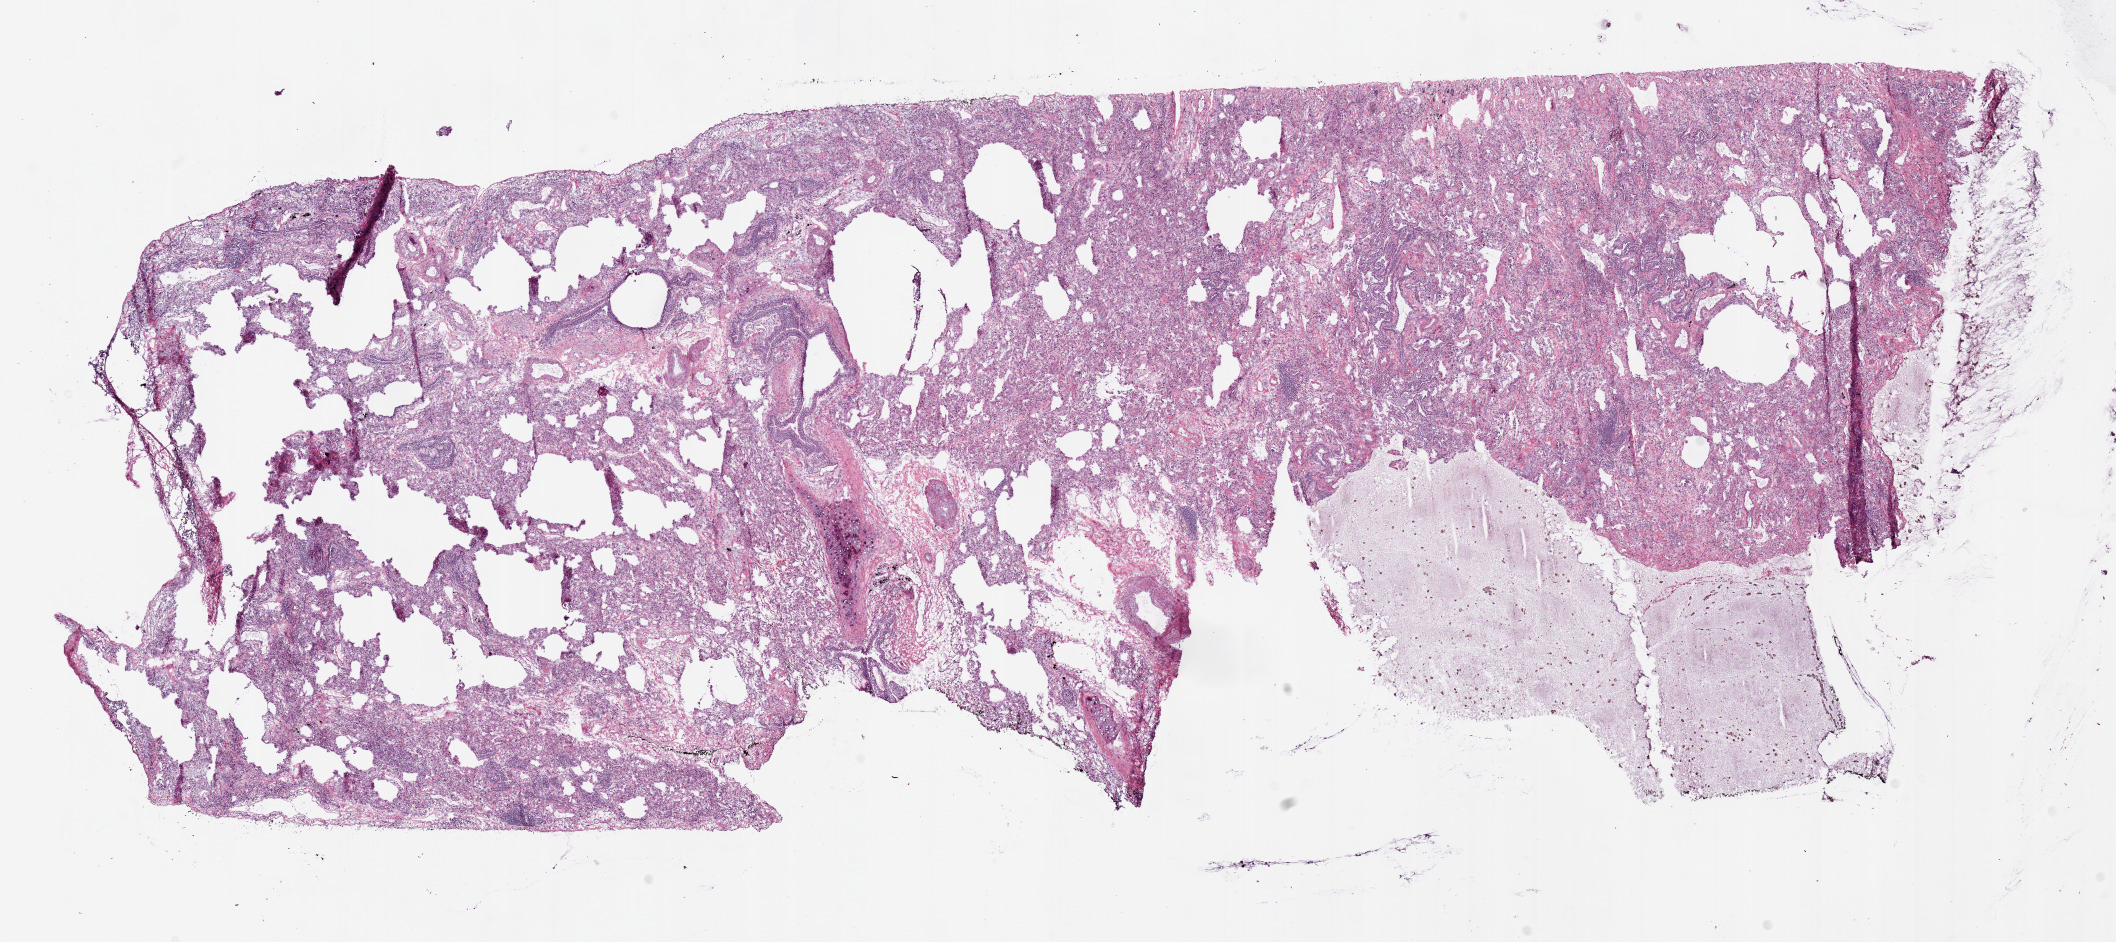
H&E-stained whole-slide image, a low-resolution overview of the entire scanned area, about 16.7 x 7.4 mm, frozen section, lung, solid tissue normal (non-tumour tissue) sample. Patient: female, age at initial diagnosis 79 years.
- this section: solid tissue normal sample (biorepository sample class)
- patient diagnosis: Adenocarcinoma, NOS